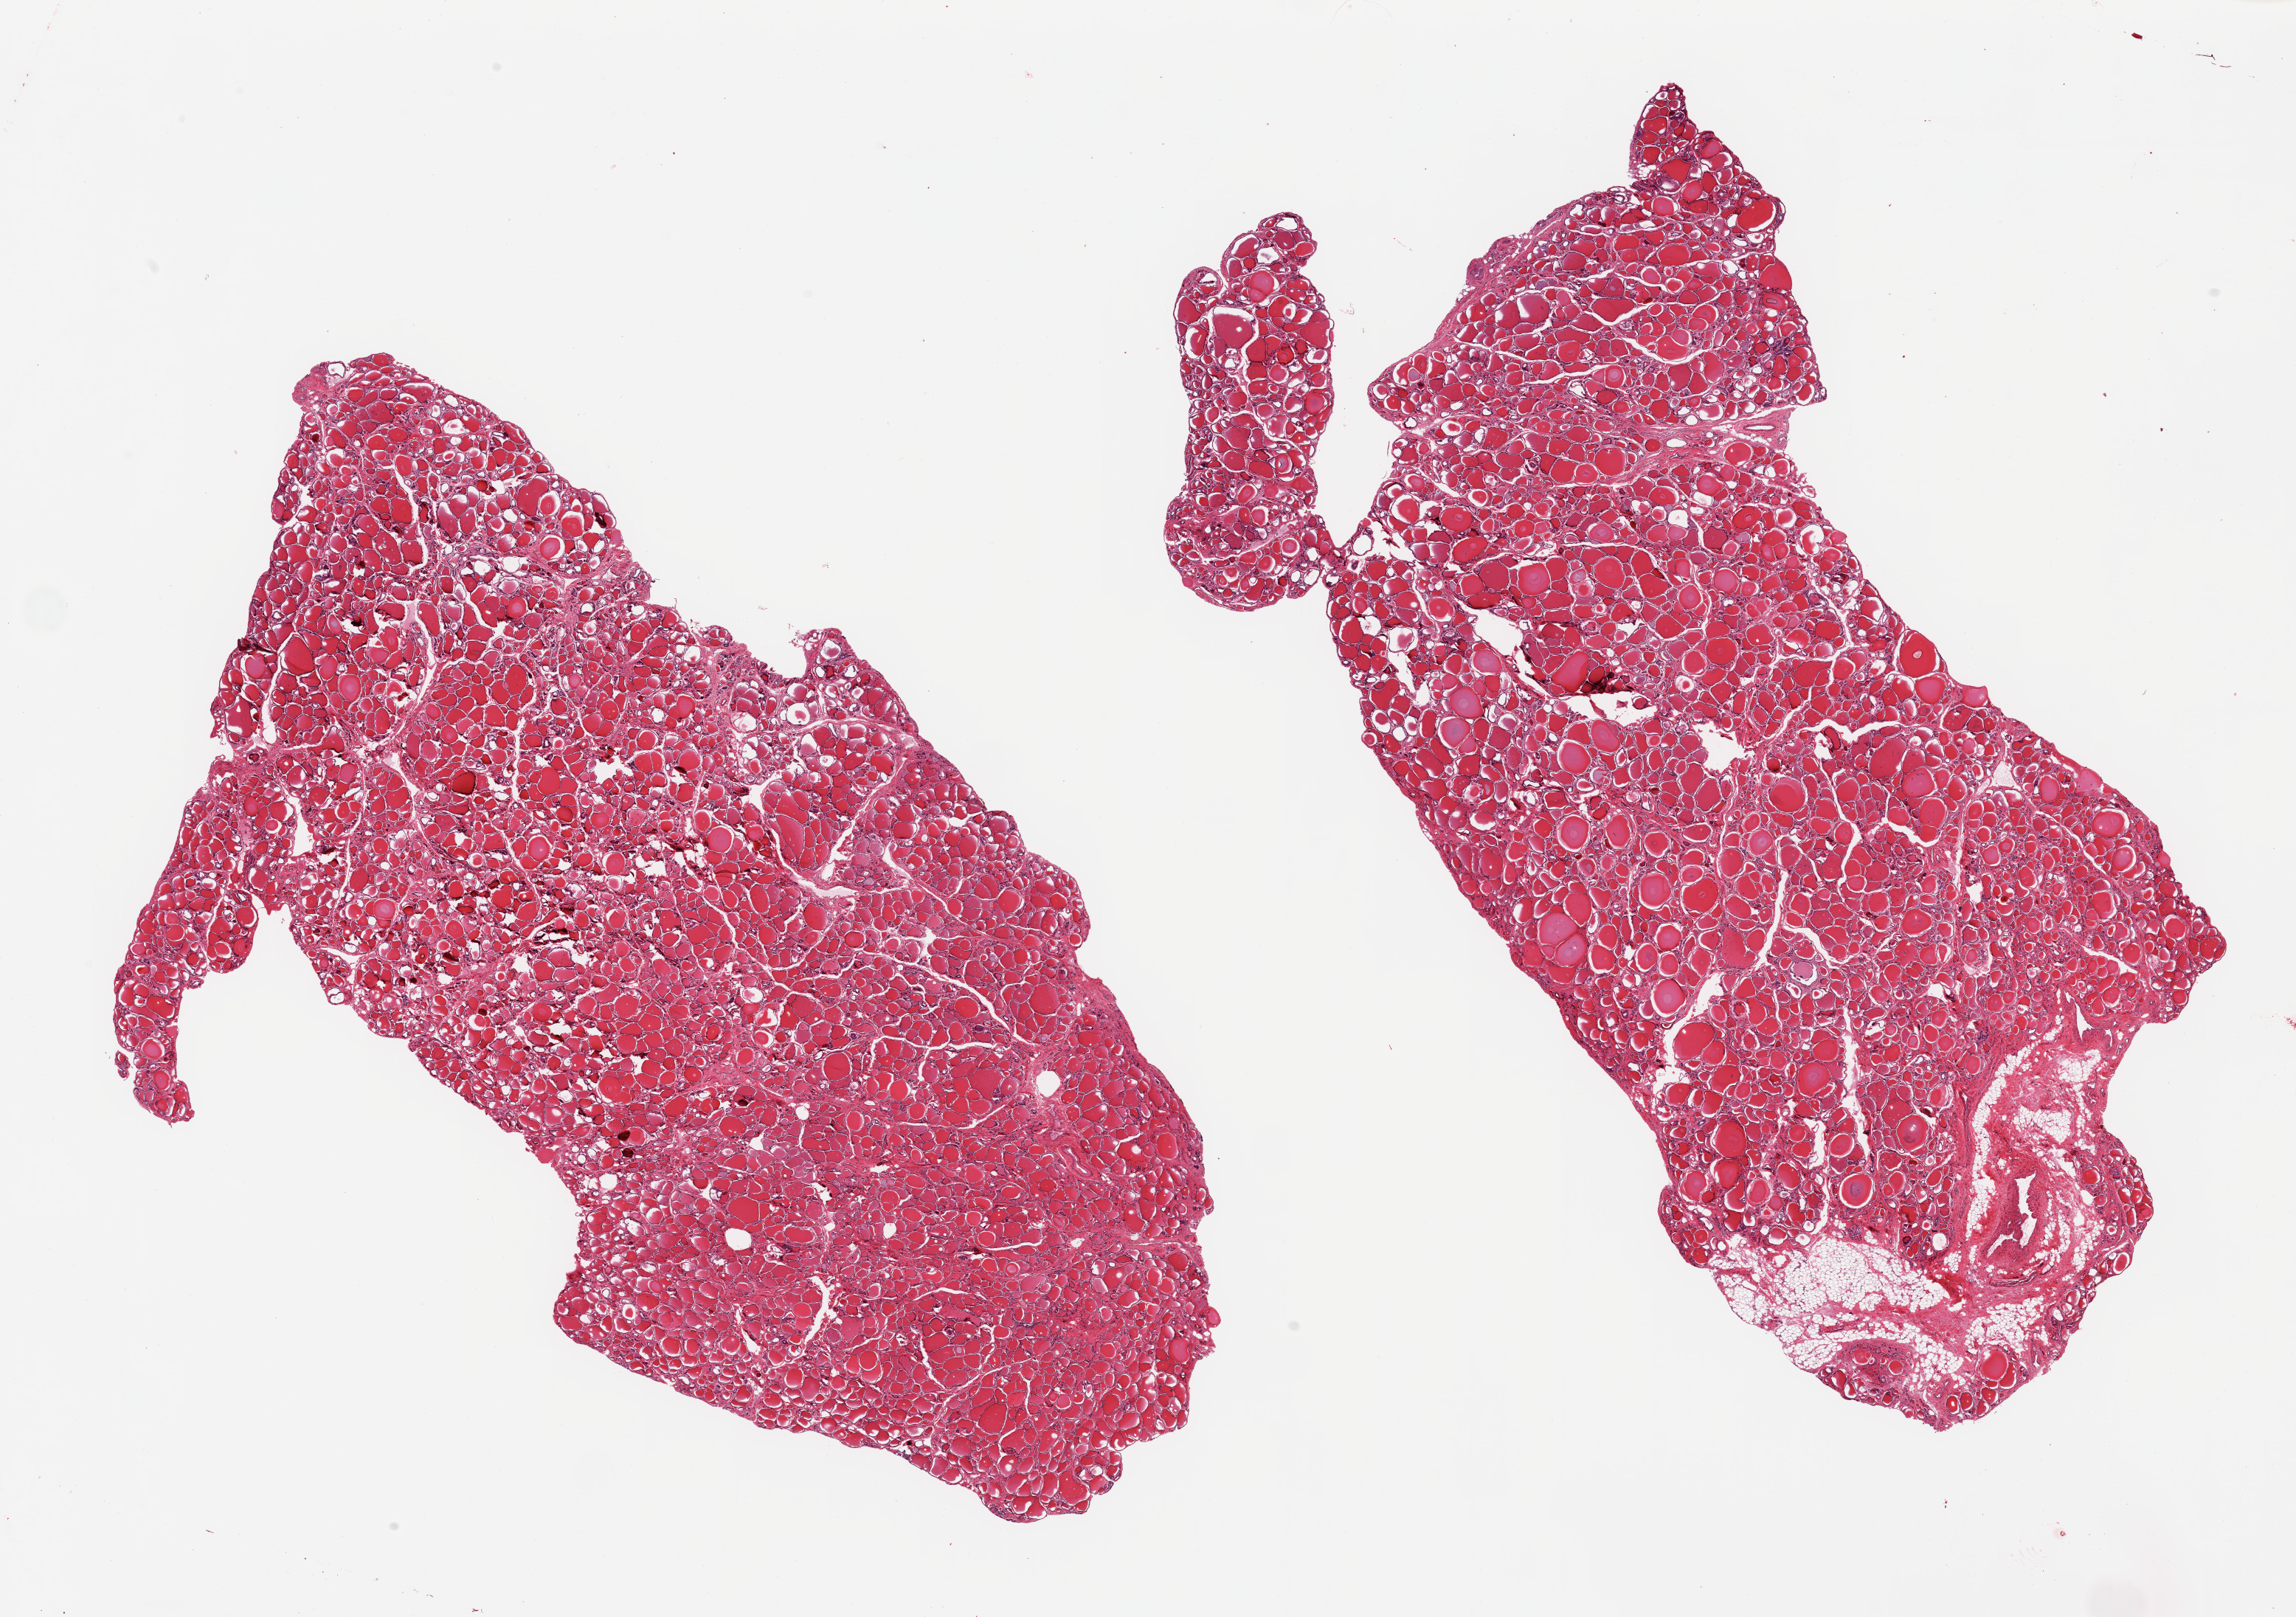
Hematoxylin and eosin (H&E) whole-slide image, brightfield, low-resolution overview of the scanned area, about 24.6 x 17.3 mm (acquisition: 20x scan), PAXgene-fixed, paraffin-embedded tissue, sampled site (target tissue): thyroid, tissue donor sample. Donor sex: male.
- review note (as recorded): 2 pieces, ~5x1mm nubbin of adherent fat/vascular tissue